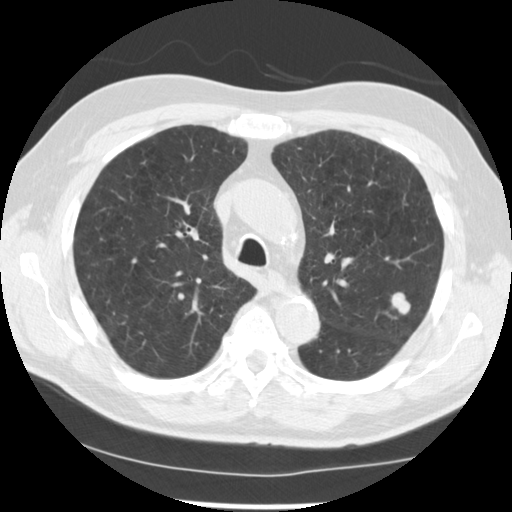
Low-dose screening chest CT, axial slice. Baseline screening round. Lung window (W 1500 / L -600 HU). Slice 172 of 249 in the series. 512 × 512 image matrix, field of view 341 × 341 mm. Male participant, aged 71 years at enrolment.
Lesion marked by an expert reader, bounding box [x1, y1, x2, y2] px = [379, 283, 425, 329]. The screening reader recorded 2 non-calcified nodules or masses ≥4 mm on this exam; which of them this box marks is not recorded. Official screen result: positive, change unspecified: nodule(s) >= 4 mm or enlarging nodule(s), mass(es), or other non-specific abnormalities suspicious for lung cancer. Later outcome: lung cancer diagnosed 37 days after this screen — adenocarcinoma, NOS, left upper lobe, poorly differentiated (G3), stage IIIB (AJCC 6th edition), 25 mm at pathology.